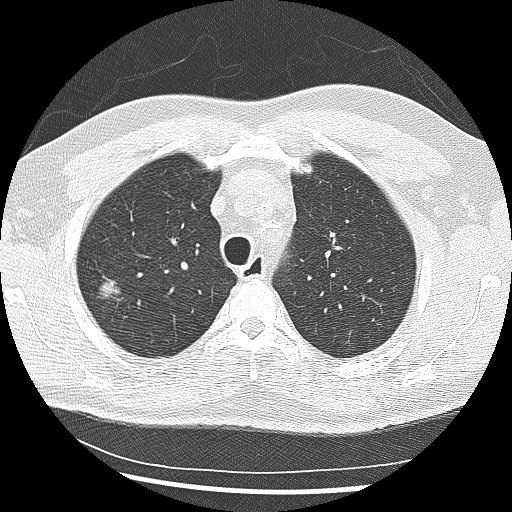
Low-dose screening chest CT, one axial slice. Position 206 of 265 along the scan axis. Reconstruction kernel LUNG. 120 kVp. Lung window (W 1500 / L -600 HU). 2.5 mm slice thickness. 512 × 512 image matrix, field of view 340 × 340 mm.
Outlined on this slice (outlined manually by an expert reader):
- lesion 1 (tumor, upper lobe of right lung): bounding box <99,282,121,298> (left, top, right, bottom; pixels)